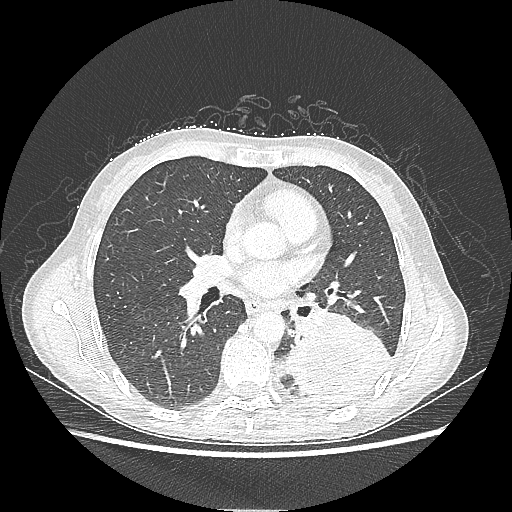
Chest CT, one axial slice; slice 116 of 220 in the series (ordered by position); reconstruction kernel LUNG; 80 kVp; lung window (W 1500 / L -600 HU); 1.25 mm slice thickness; 512 × 512 image matrix. Female patient, age 53 years. From the clinical record (not read from this slice): clinical TNM (as recorded): T3 N0 M0.
Outlined on this slice (bounding box drawn by a radiologist):
- lung tumour (recorded histology: adenocarcinoma): box from (x=286, y=312) to (x=390, y=409) px